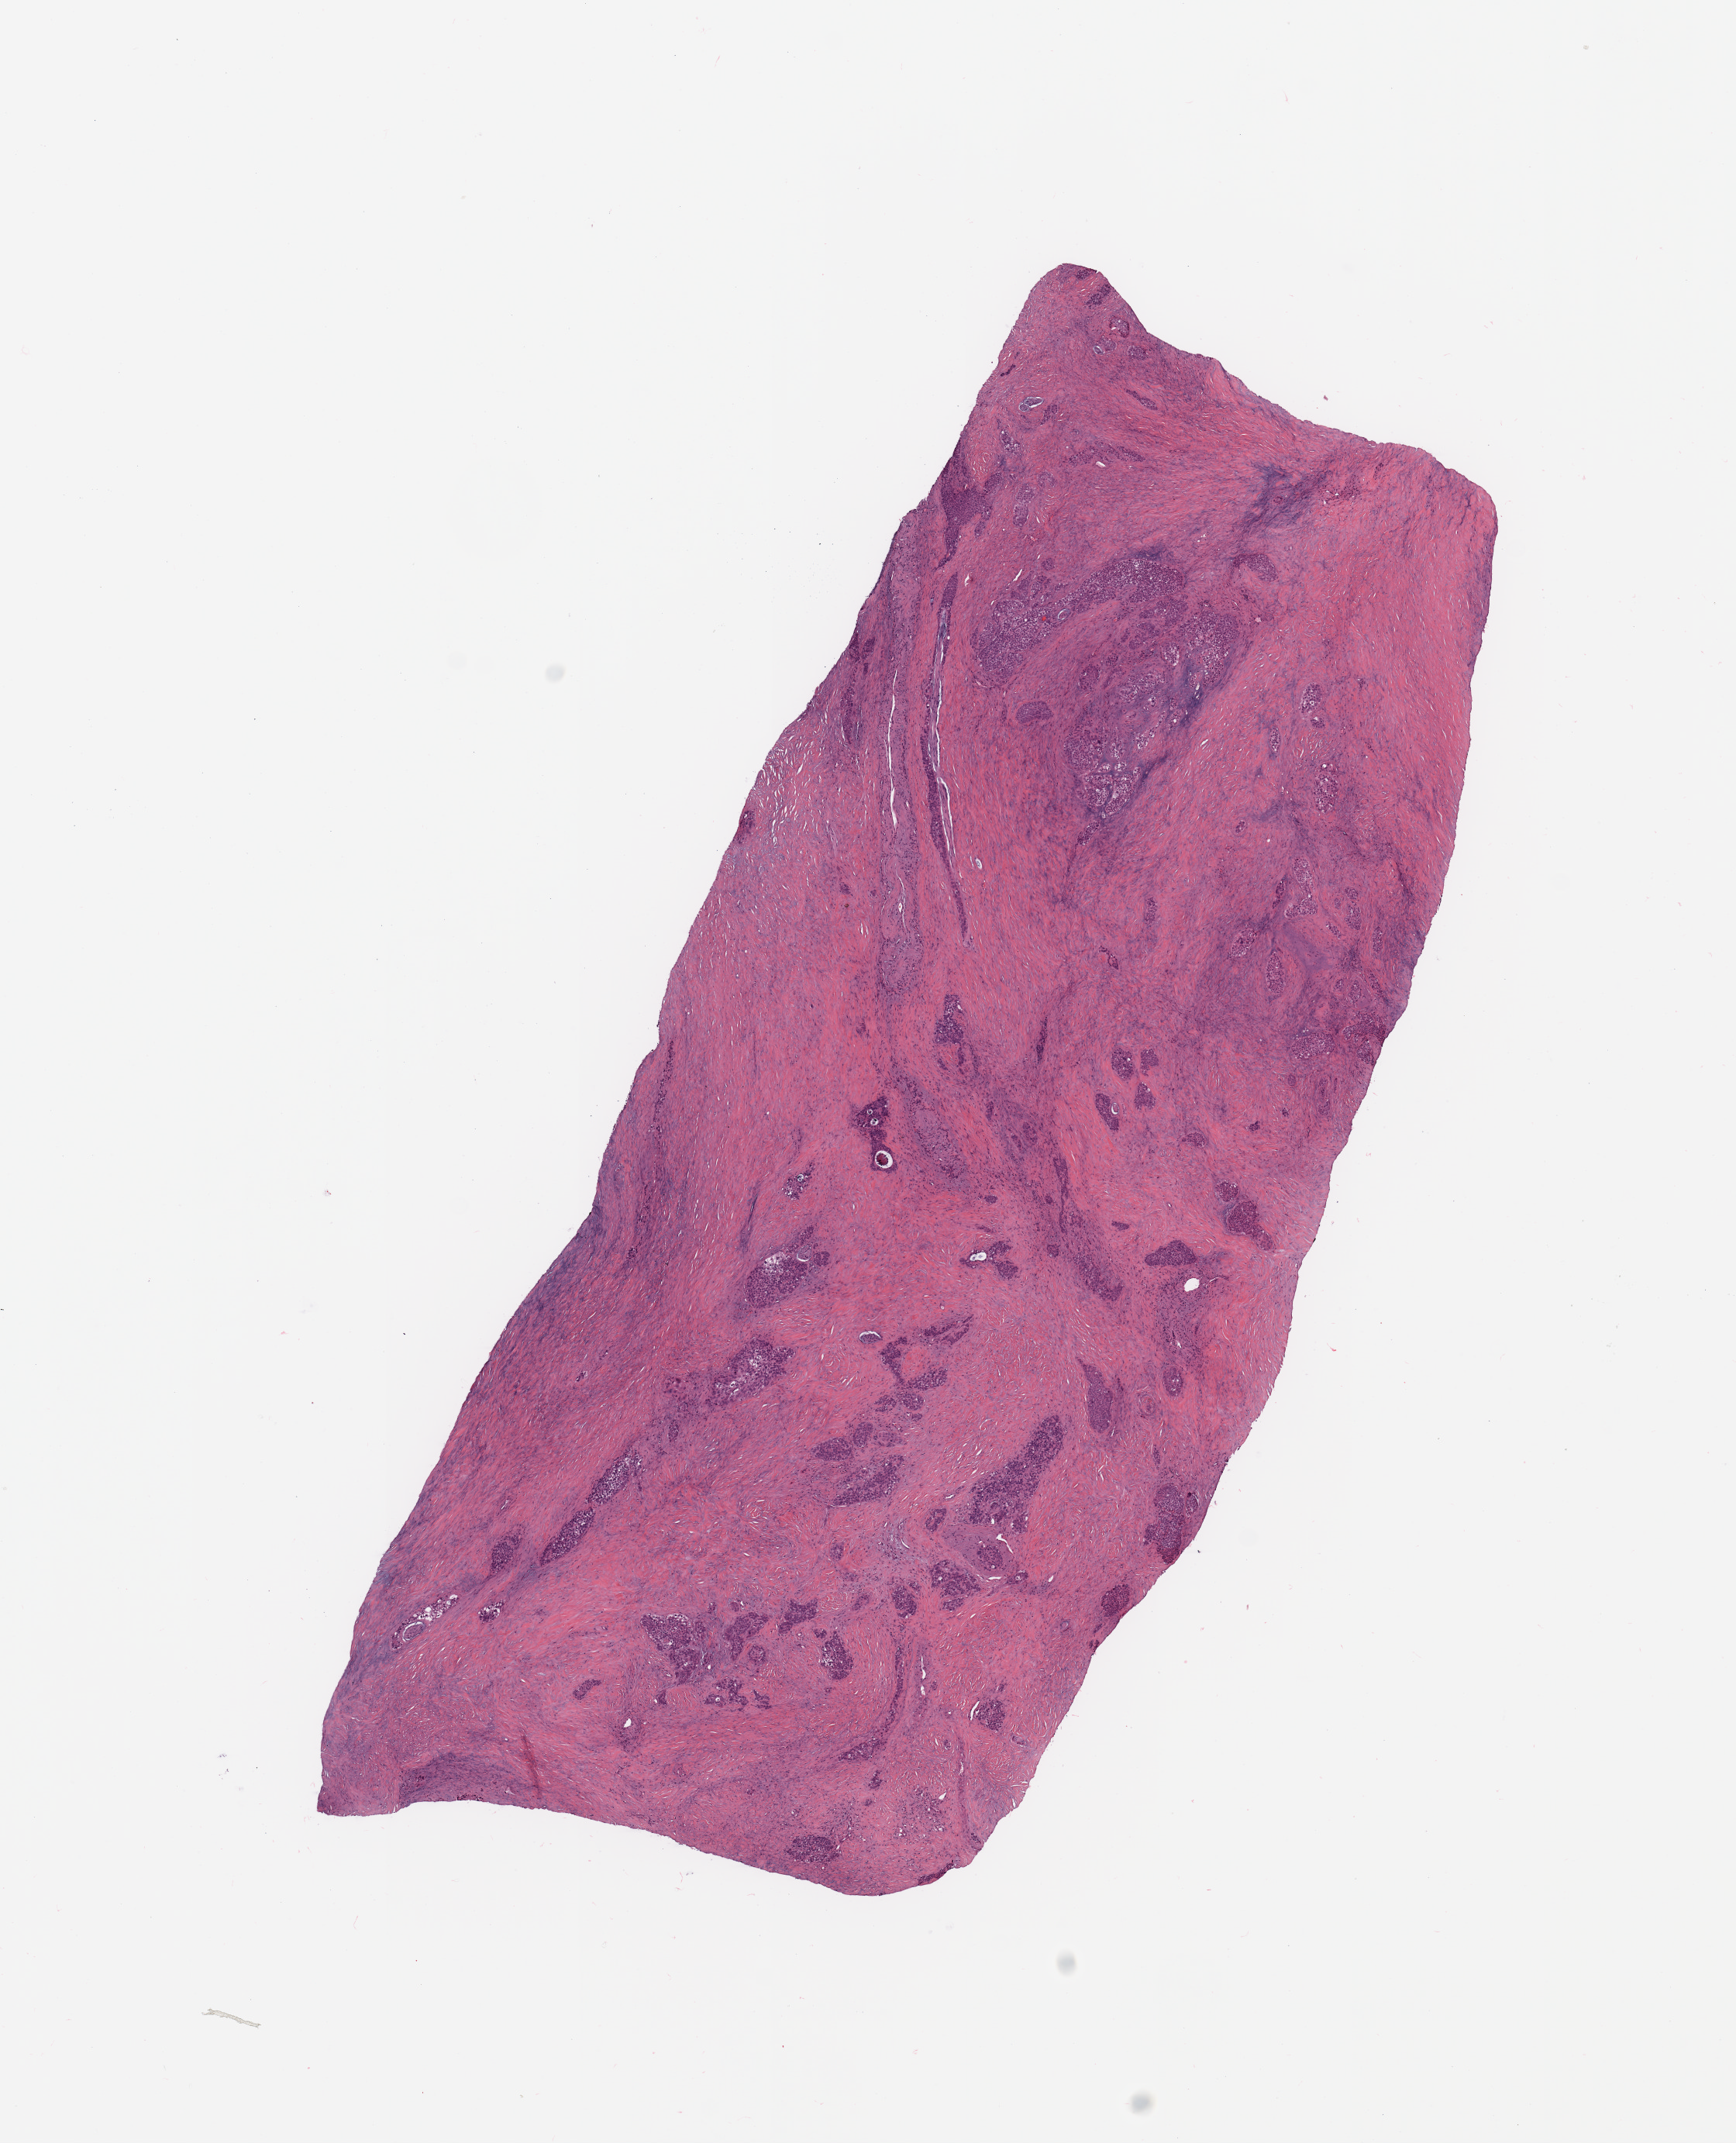
Hematoxylin and eosin (H&E) stained whole-slide image, a low-resolution overview of the entire scanned area, about 8.9 x 10.9 mm. Tumour tissue sample, sampled site: pancreas. Patient: male, age 69 years. Histologic grade: G2 (moderately differentiated). Pathologist review of this section (percent, as recorded): tumour nuclei 50%, necrosis 0%.
* diagnosis: Infiltrating duct carcinoma, NOS
* AJCC pathologic stage: IIA
* primary tumour site (as recorded): tail